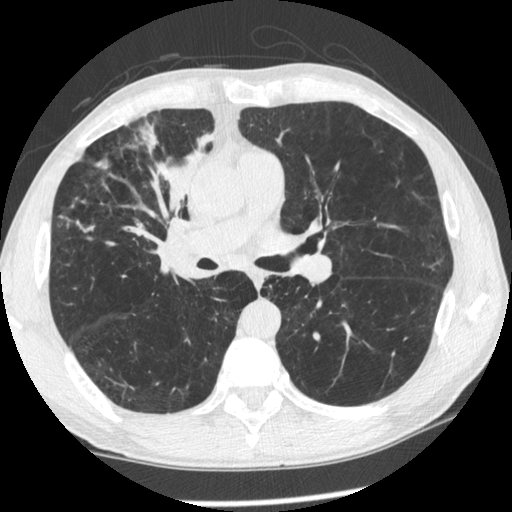
Low-dose screening chest CT, one axial slice. Reconstruction kernel STANDARD. 120 kVp. Lung window (W 1500 / L -600 HU). 1.25 mm slice thickness. 512 × 512 image matrix, field of view 340 × 340 mm.
Outlined on this slice (expert manual segmentation):
- lesion 1 (tumor, upper lobe of right lung): bounding box <150,134,213,237> (left, top, right, bottom; pixels)